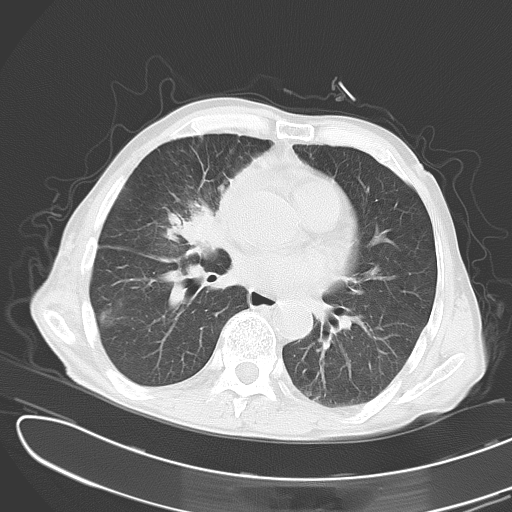
Chest CT, one axial slice; slice 15 of 43 in the series (ordered by position); reconstruction kernel B70f; 120 kVp; lung window (W 1500 / L -600 HU); 512 × 512 image matrix. Patient: male, 65 years. Case-level facts recorded for this patient, not image findings: clinical TNM (as recorded): T2 N3 M1; histopathological grade: G3.
Outlined on this slice (rectangle marked by the reading radiologist):
- lung tumour (recorded histology: small cell carcinoma): bounding box <182,153,284,249> (left, top, right, bottom; pixels)